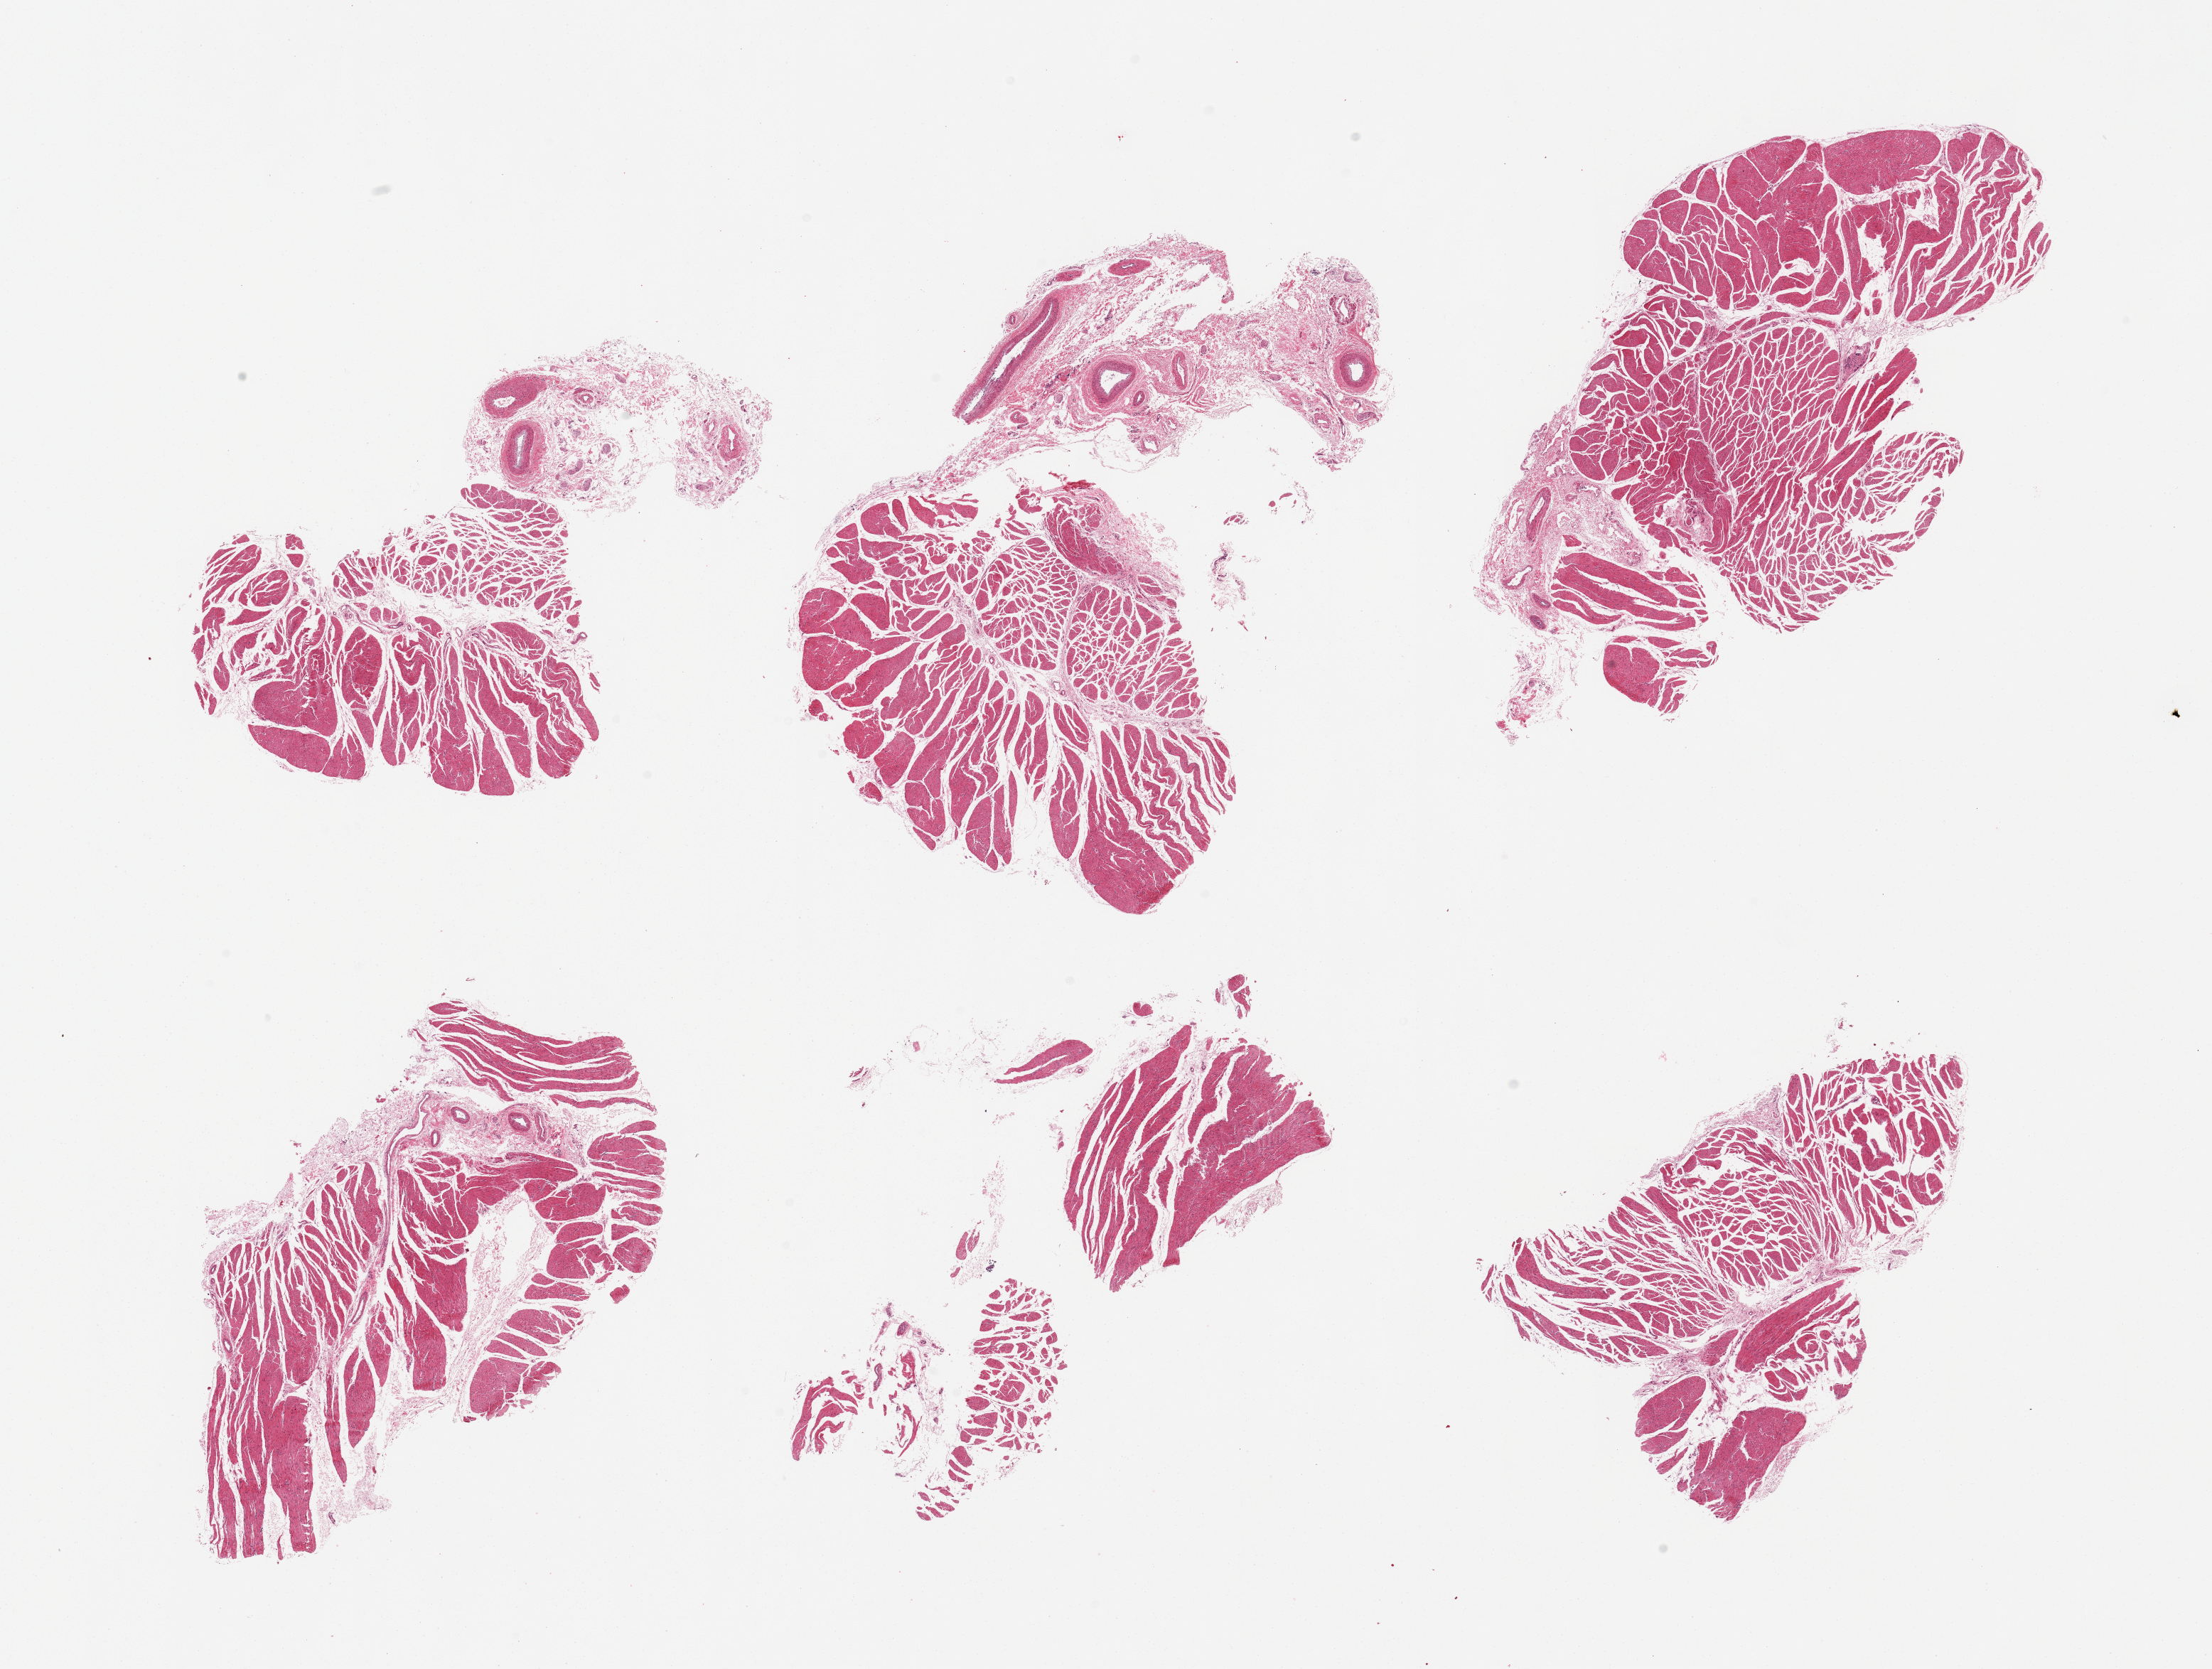
Hematoxylin and eosin (H&E) whole-slide image, shown as a low-resolution overview of the whole scanned area (about 24.6 x 18.6 mm, from a 20x scan). PAXgene-fixed paraffin-embedded (PFPE) section. Sampled site (target tissue): esophageal muscle. Donor tissue sample. Donor sex: female.
Review note (as recorded): 6 pieces with up to 40% submucosal fibrovascular stroma.